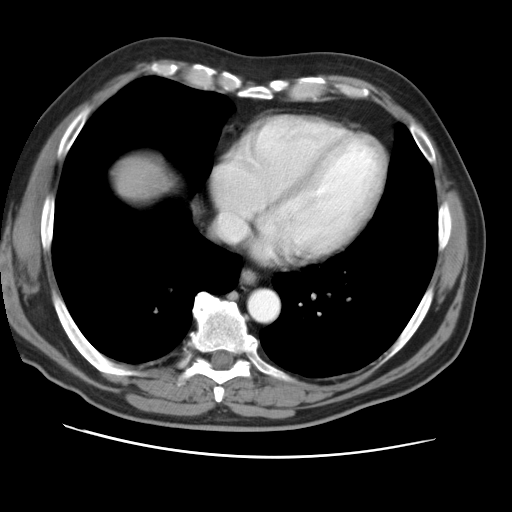
Contrast-enhanced abdominal CT, one axial slice; slice 48 of 49 in the series (ordered by position); reconstruction kernel STANDARD; 120 kVp; intravenous contrast given; soft-tissue window (W 400 / L 40 HU); 5 mm slice thickness; 512 × 512 image matrix. Male patient, age 59 years. From the clinical record (not read from this slice): diagnosis: colorectal cancer liver metastases, imaged before liver resection; multiple liver metastases: yes; largest metastasis: 6.3 cm.
Annotated regions visible in this slice (outlined manually by an expert reader):
- liver: box from (x=119, y=161) to (x=167, y=196) px
- planned liver remnant (the part of the liver to remain after resection): (x=119, y=161)–(x=164, y=195)